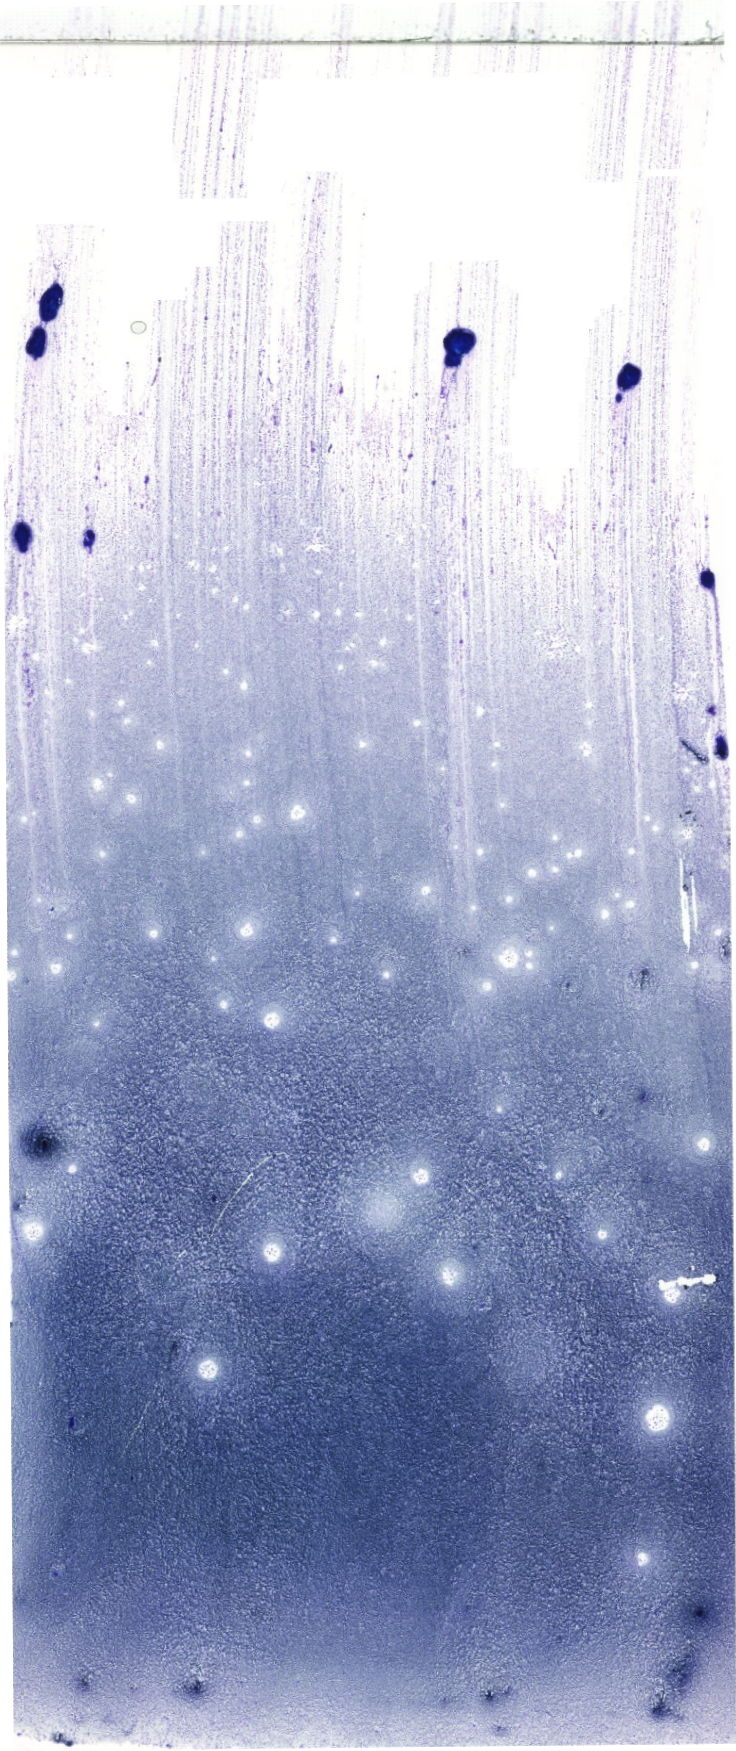
Whole-slide image of a May-Grünwald–Giemsa-stained bone marrow aspirate smear, whole scanned area (about 20.9 x 49.6 mm) shown as a low-resolution overview. Female patient.
Diagnosis: B Acute Lymphoblastic Leukemia.